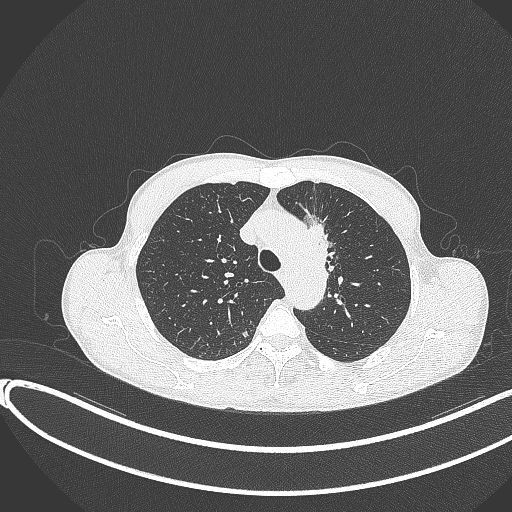
Chest CT, one axial slice; slice 285 of 374 in the series (ordered by position); lung window (W 1500 / L -600 HU); 1 mm slice thickness; 512 × 512 image matrix, field of view 400 × 400 mm. Male patient, age 58 years. Case-level facts recorded for this patient, not image findings: clinical TNM (as recorded): T1c N1 M0.
Structures marked on this image (rectangle marked by the reading radiologist):
- lung tumour (recorded histology: adenocarcinoma): bounding box <301,215,335,266> (left, top, right, bottom; pixels)